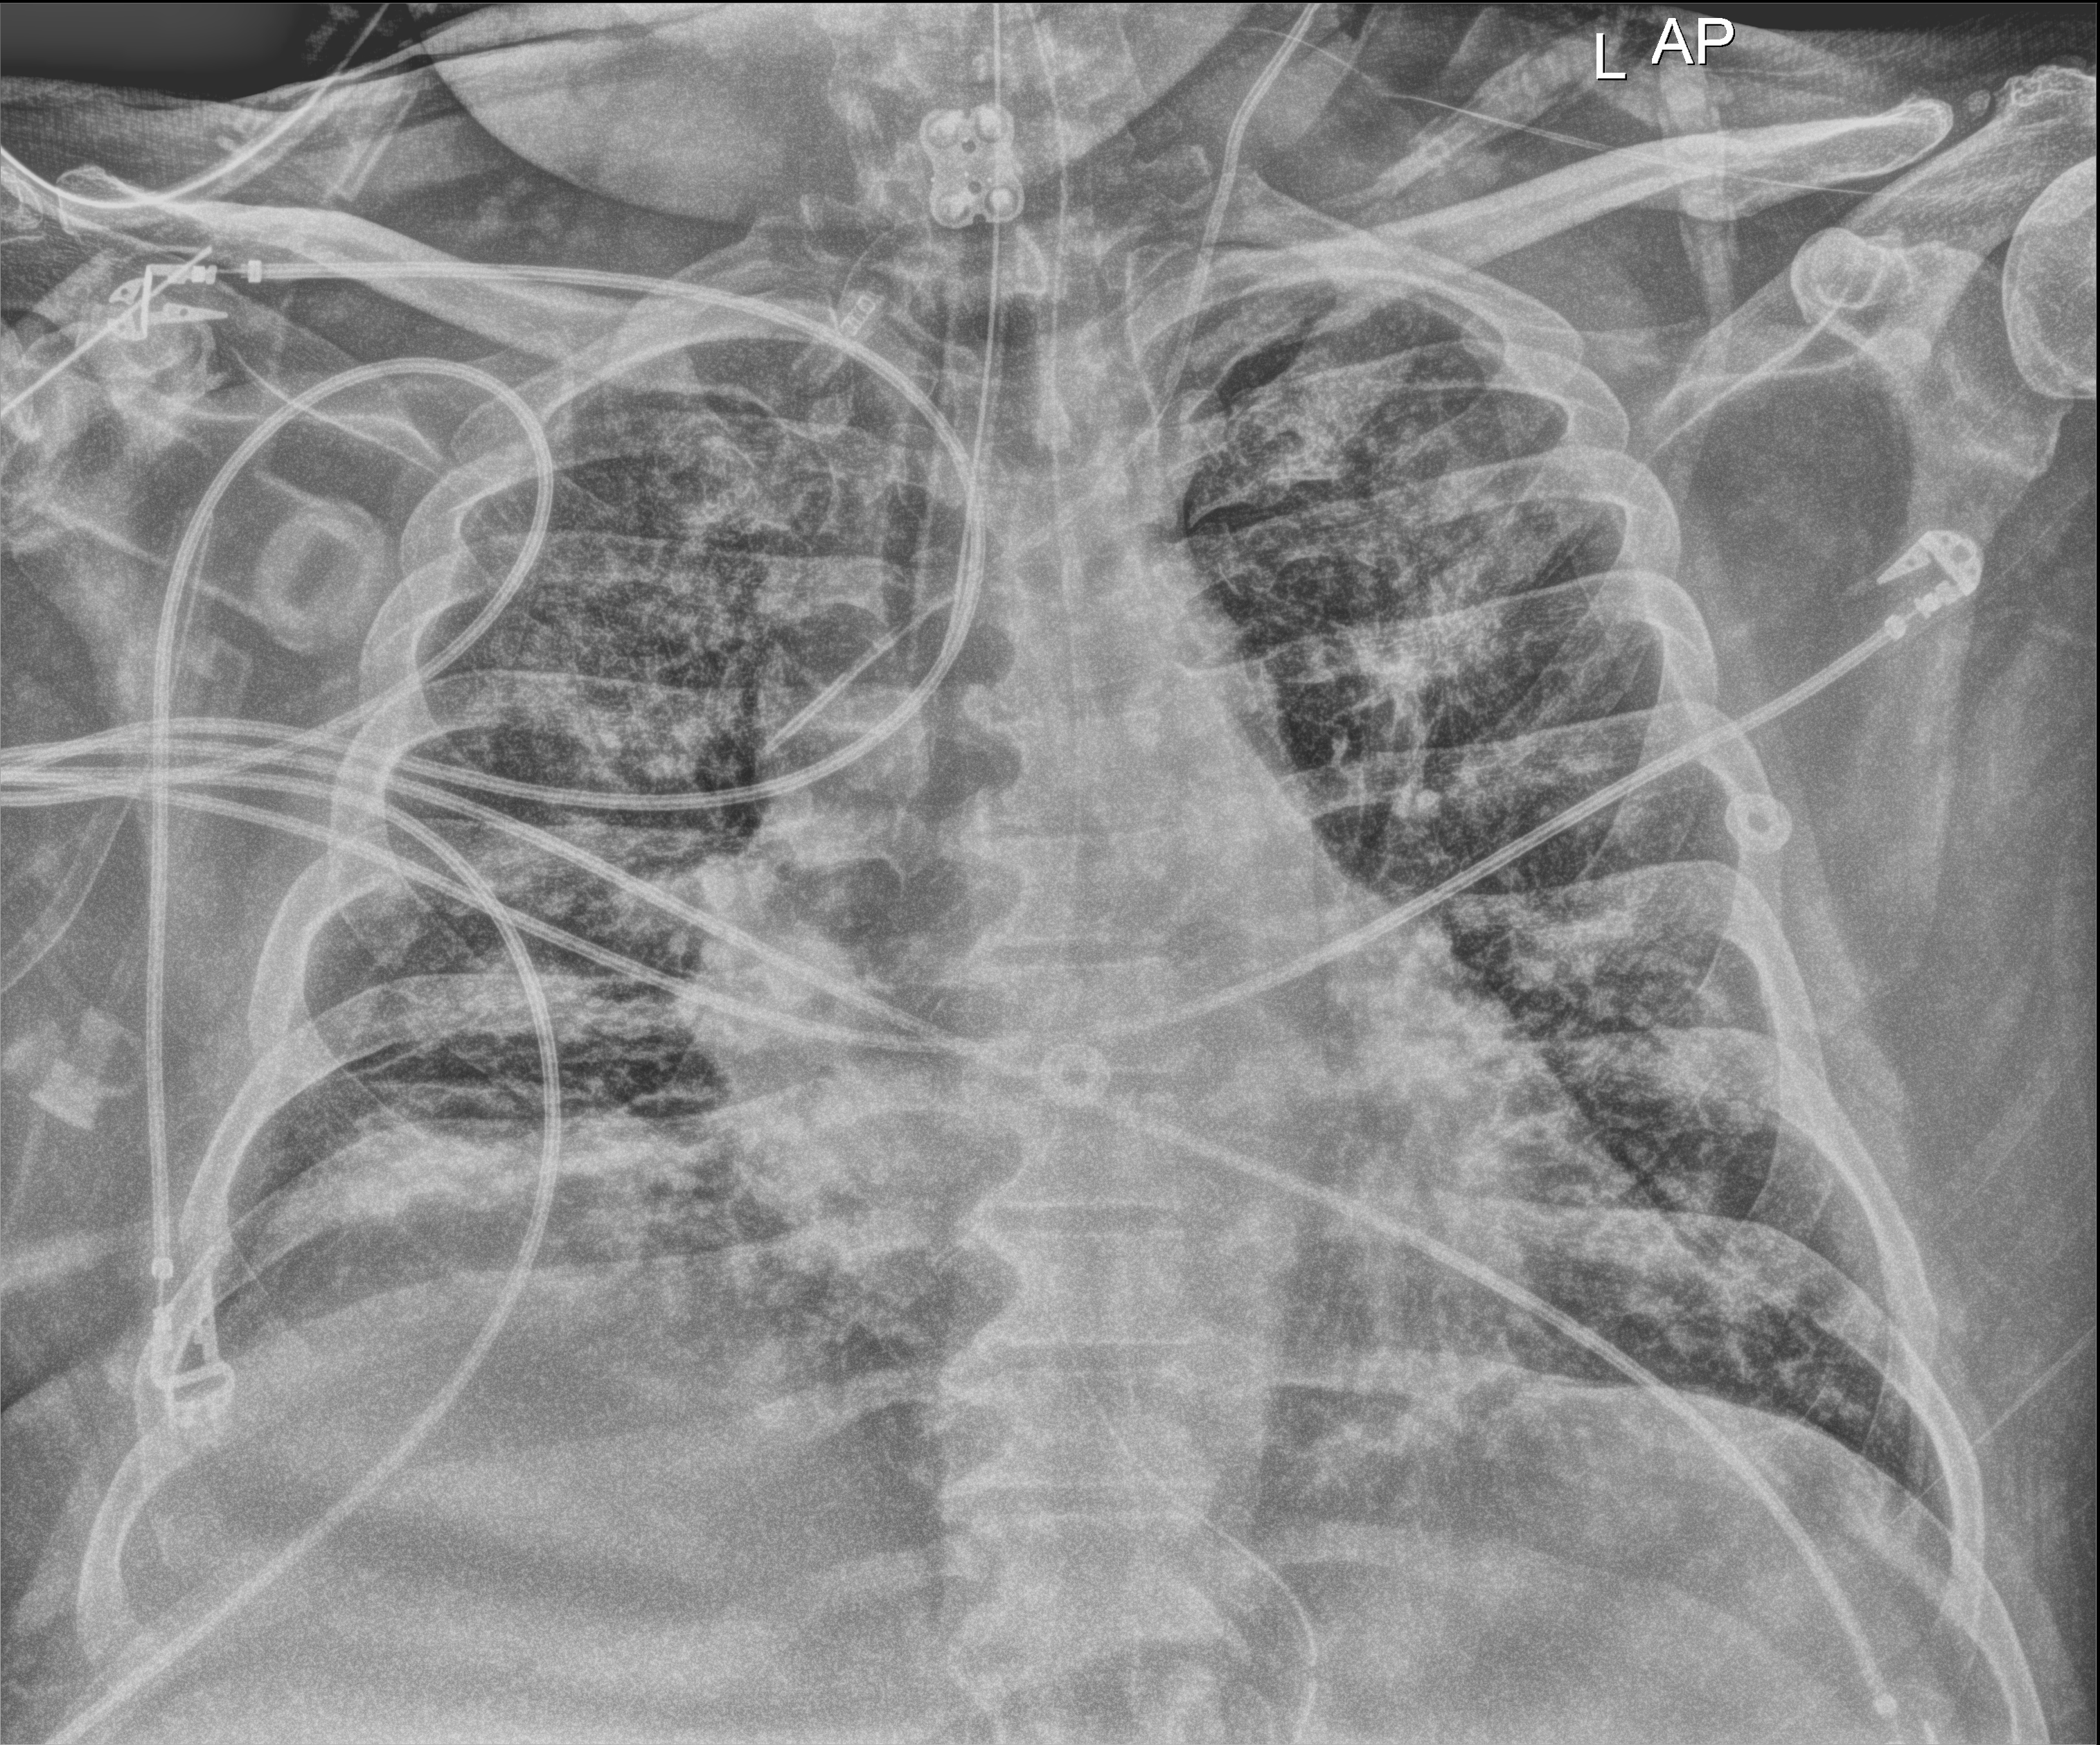
Bedside chest radiograph (digital radiography), anteroposterior (AP) projection. Patient hospitalised with COVID-19; male, aged 18–59 years.
Admission-level facts for this patient (not findings on this image; timing relative to this image not recorded):
- length of hospital stay: 47 days